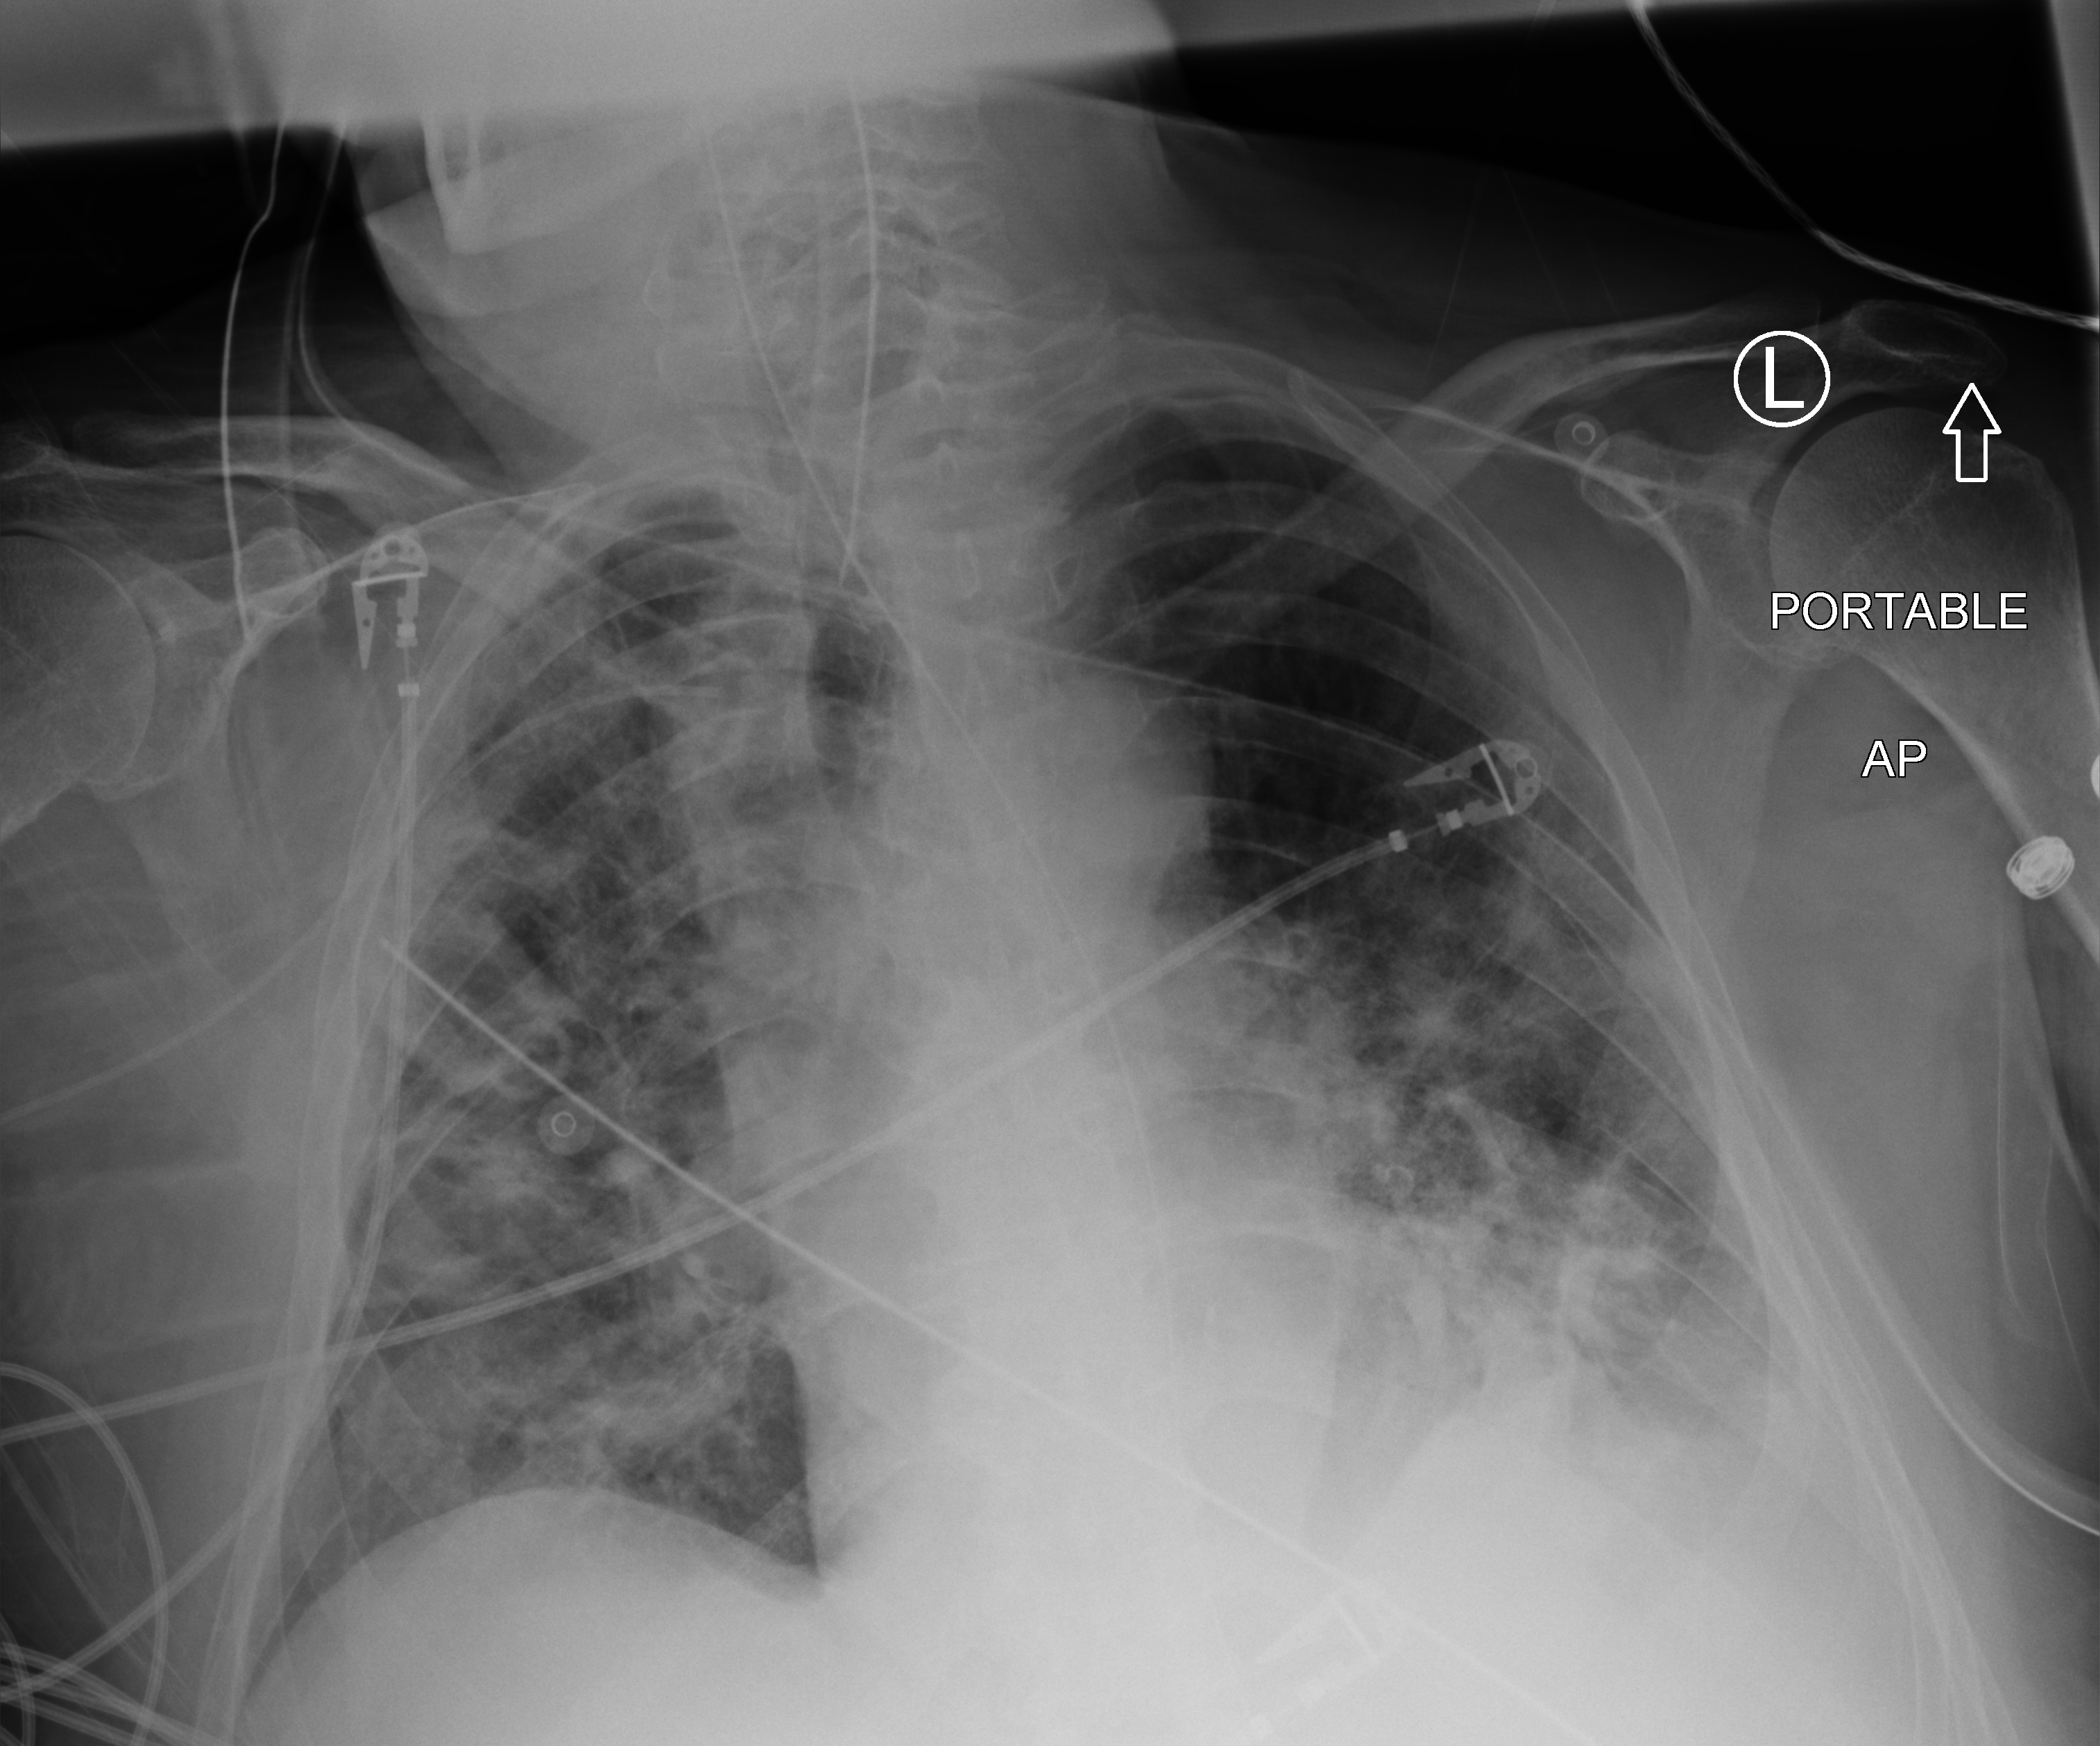
Chest X-ray (portable), anteroposterior (AP) projection. Patient hospitalised with COVID-19; male, aged 60–74 years.
From the hospital-stay record, not from the radiograph (when in the stay this image was taken is not recorded):
- COPD (admission record): no
- admitted to intensive care during this hospital stay: yes